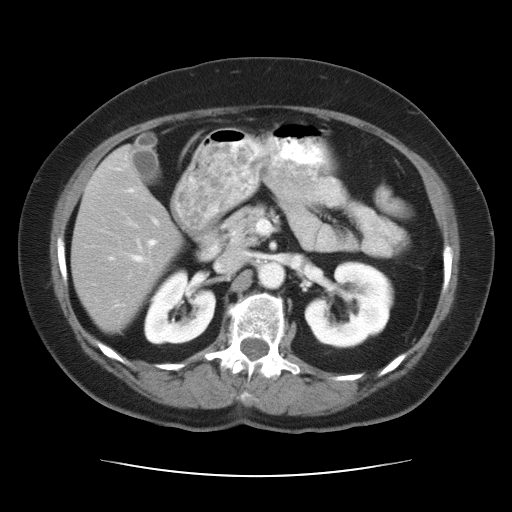
Contrast-enhanced abdominal CT, one axial slice. Reconstruction kernel STANDARD. 120 kVp. Soft-tissue window (W 400 / L 40 HU). 7.5 mm slice thickness. 512 × 512 image matrix, field of view 360 × 360 mm. Female patient, age 65 years. Case-level facts recorded for this patient, not image findings: diagnosis: colorectal cancer liver metastases, imaged before liver resection; multiple liver metastases: yes; largest metastasis: 2.2 cm; disease in both lobes: no.
Structures marked on this image (outlined manually by an expert reader):
- hepatic veins: box from (x=125, y=188) to (x=260, y=272) px
- liver: (x=73, y=150)–(x=181, y=329)
- planned liver remnant (the part of the liver to remain after resection): (x=73, y=150)–(x=181, y=329)
- portal vein (with intrahepatic branches): (x=128, y=218)–(x=159, y=247)